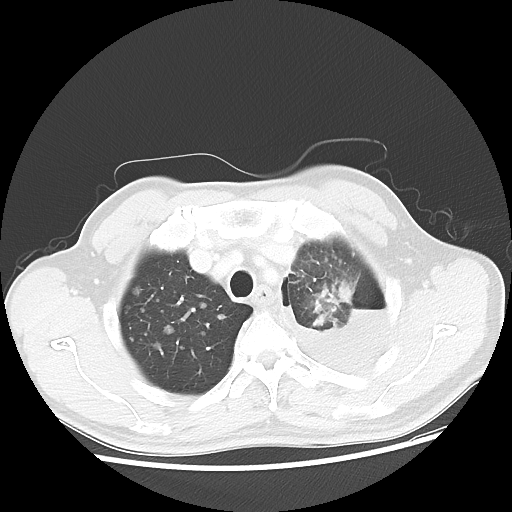
Chest CT, one axial slice. Position 40 of 47 along the scan axis. Lung window (W 1500 / L -600 HU). 512 × 512 image matrix. Patient: male, 55 years. From the clinical record (not read from this slice): clinical TNM (as recorded): T2 N3 M1a.
Annotated regions visible in this slice (bounding box drawn by a radiologist):
- lung tumour (recorded histology: squamous cell carcinoma): bounding box (x1, y1, x2, y2) in pixels: (303, 276, 359, 318)